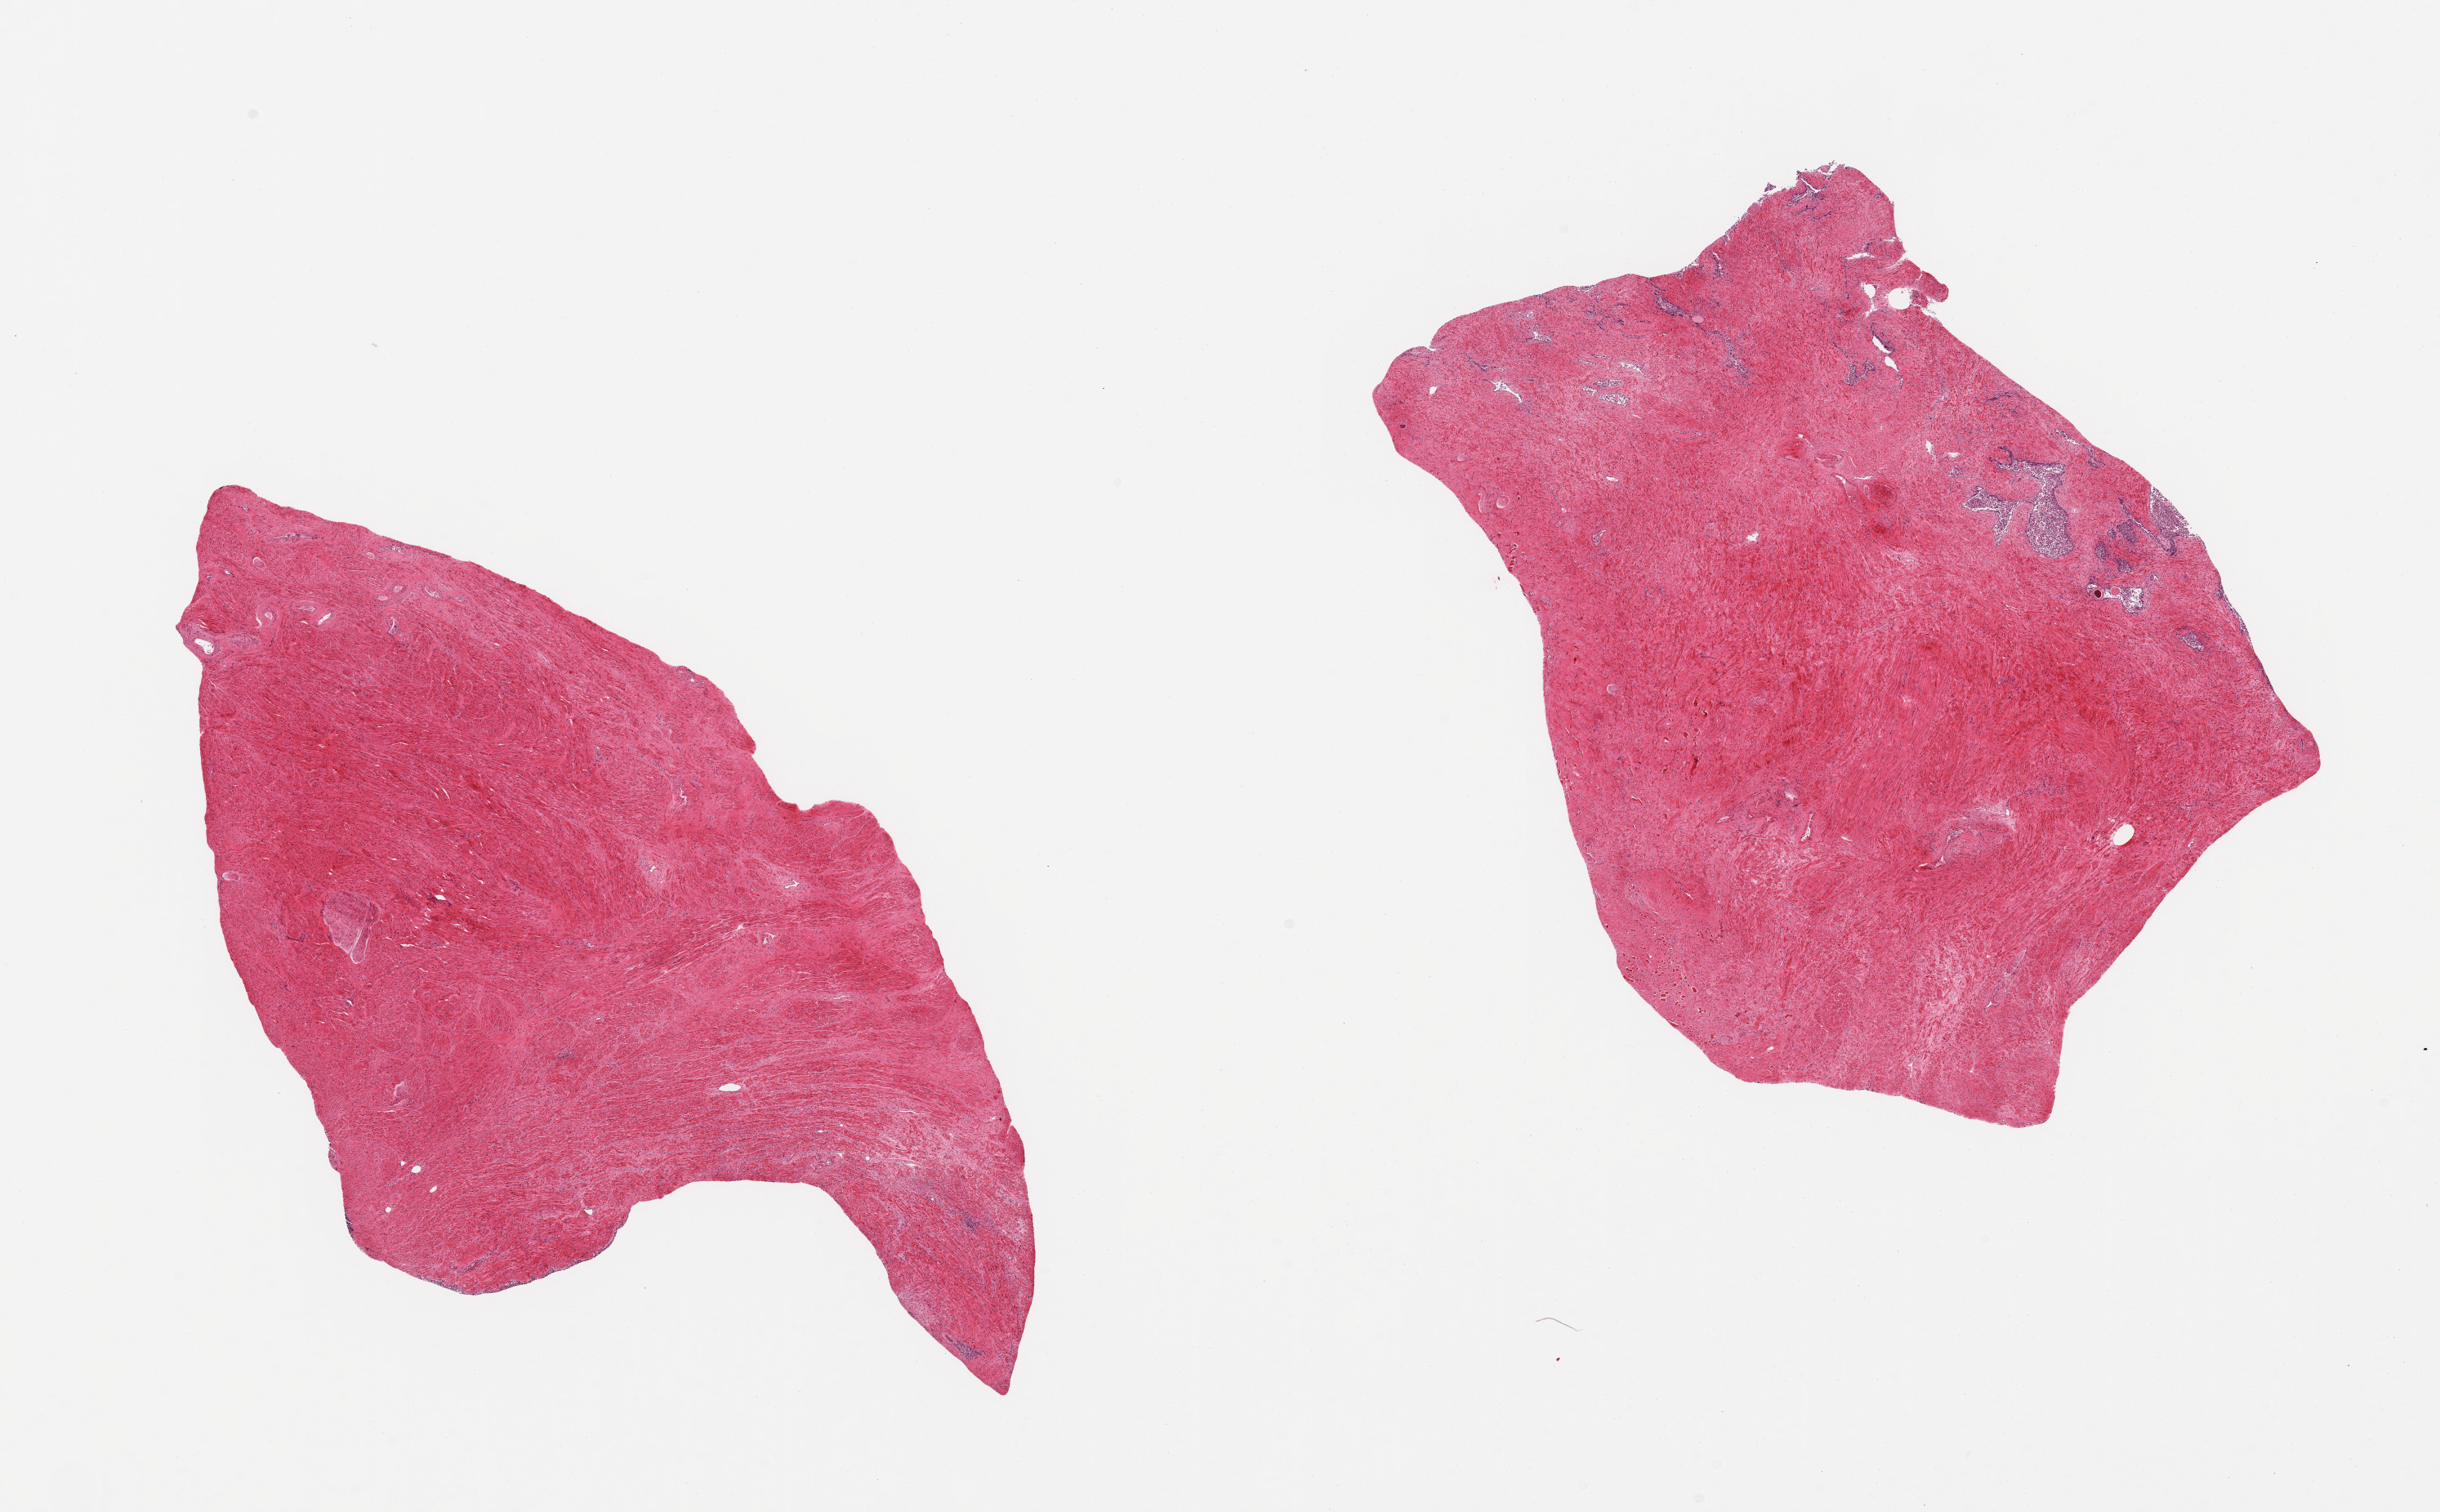
Digitized haematoxylin and eosin-stained section — whole scanned area (about 23.6 x 14.6 mm, slide scanned at 20x) shown as a low-resolution overview. PAXgene-fixed paraffin-embedded (PFPE) section. Section of prostate (target tissue). Donor tissue sample. Male donor.
Review note (as recorded): 2 pieces; 1 piece is all stroma, 2nd is 80% stroma with some glands with sloughing epithelium, focal skeletal muscle.